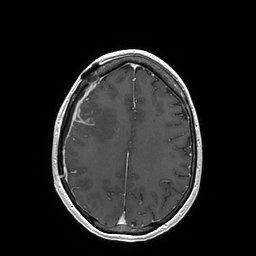
Brain MRI from a brain-tumour surgery series, one axial slice. Slice 61 of 202 in the series (ordered by position). T1-weighted post-contrast. 256 × 256 image matrix. Case-level facts recorded for this patient, not image findings: histopathology: Glioblastoma; WHO grade: 4; IDH mutation: no; tumour location: Right Insular.
Structures marked on this image (manually delineated by an expert):
- tumour: box from (x=76, y=110) to (x=91, y=125) px